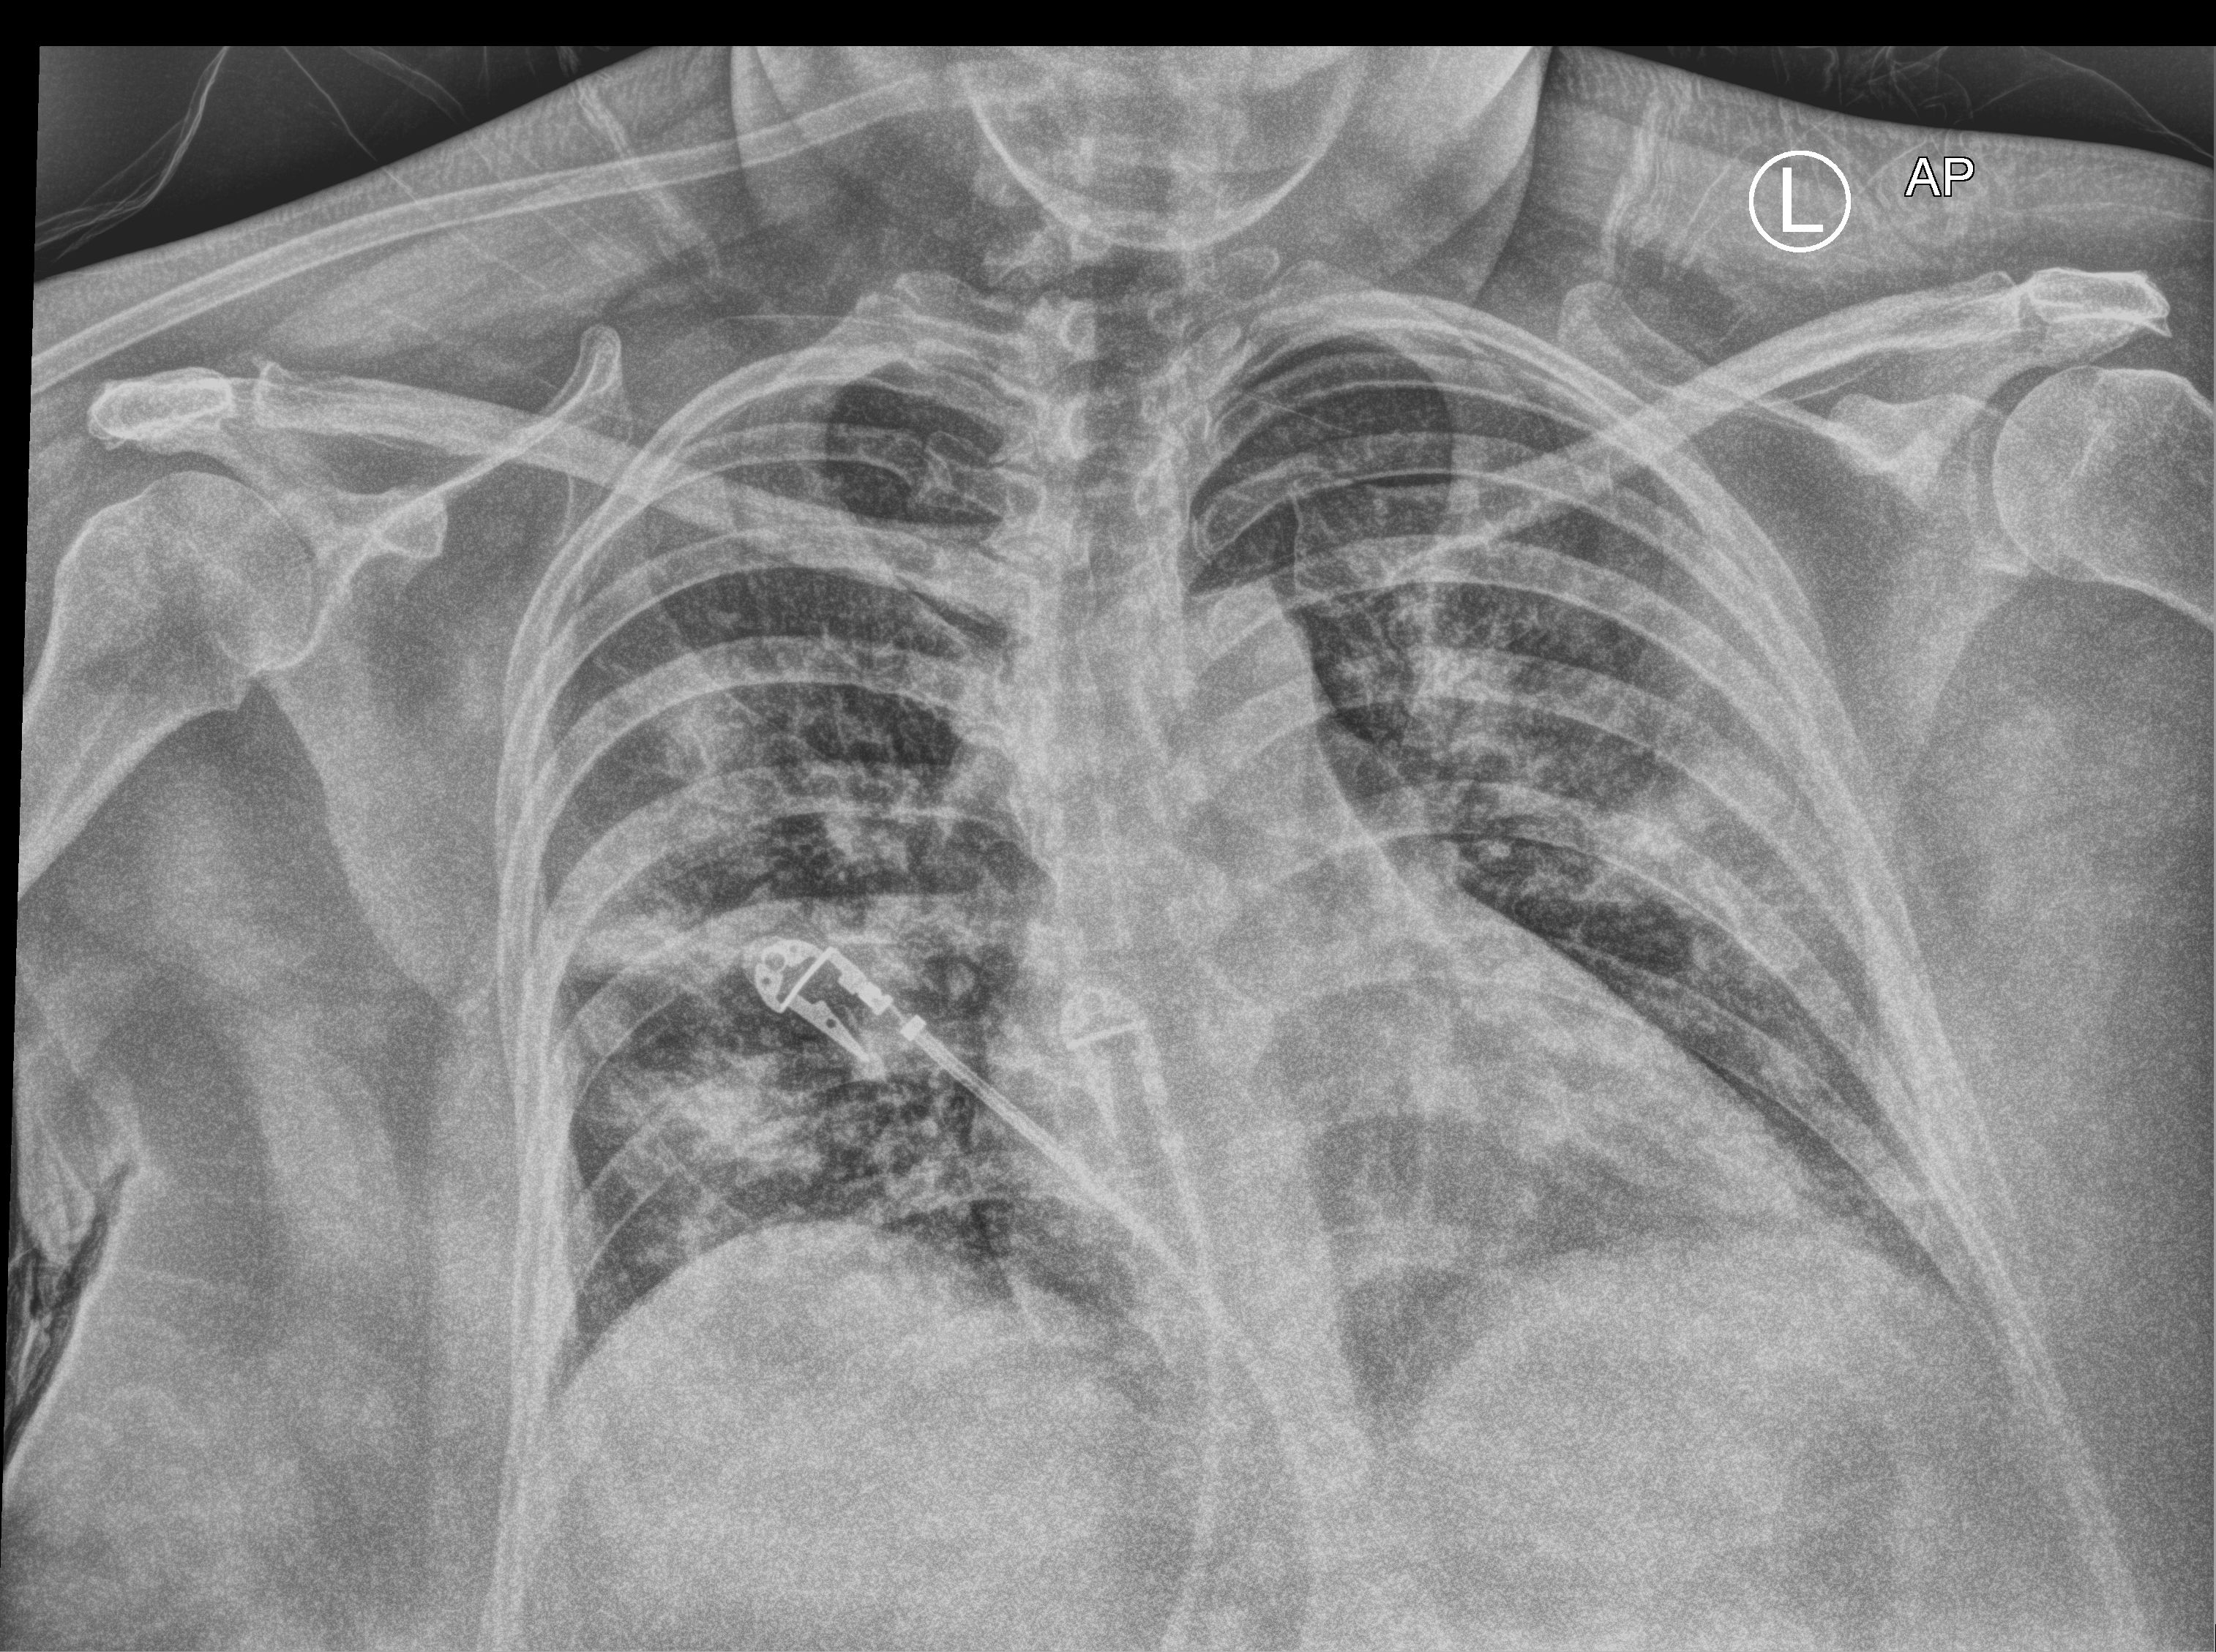
Portable chest radiograph, anteroposterior (AP) projection. Patient hospitalised with COVID-19; female, aged 18–59 years.
Admission-level facts for this patient (not findings on this image; timing relative to this image not recorded):
- mechanically ventilated during this hospital stay: no